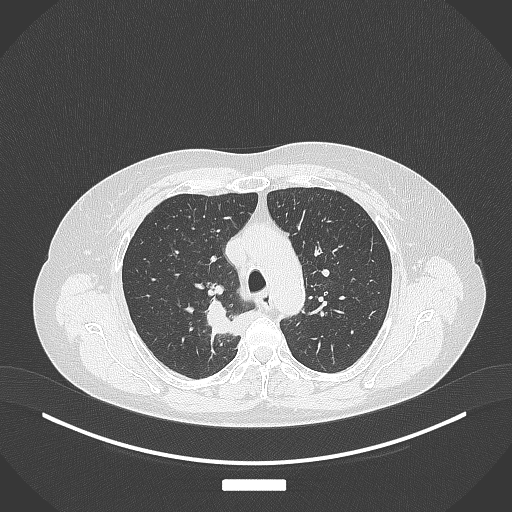
Chest CT, one axial slice; slice 280 of 357 in the series (ordered by position); reconstruction kernel B70f; lung window (W 1500 / L -600 HU); 1 mm slice thickness; 512 × 512 image matrix, field of view 400 × 400 mm. Patient: female, 62 years. Case-level facts recorded for this patient, not image findings: clinical TNM (as recorded): T1c N1 M0.
Outlined on this slice (rectangle marked by the reading radiologist):
- lung tumour (recorded histology: squamous cell carcinoma): box from (x=201, y=299) to (x=262, y=346) px